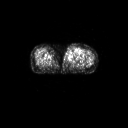
FDG PET of an extremity soft-tissue mass (from a PET/CT study), one axial slice; 128 × 128 image matrix, field of view 700 × 700 mm. Female patient, age 74 years. Case-level facts recorded for this patient, not image findings: histological type: pleomorphic leiomyosarcoma; grade: high; site of the primary tumour: left thigh.
Outlined on this slice (expert contour drawn on MRI and transferred to this co-registered scan by the dataset authors):
- gross tumour volume including surrounding oedema: box from (x=65, y=47) to (x=79, y=61) px